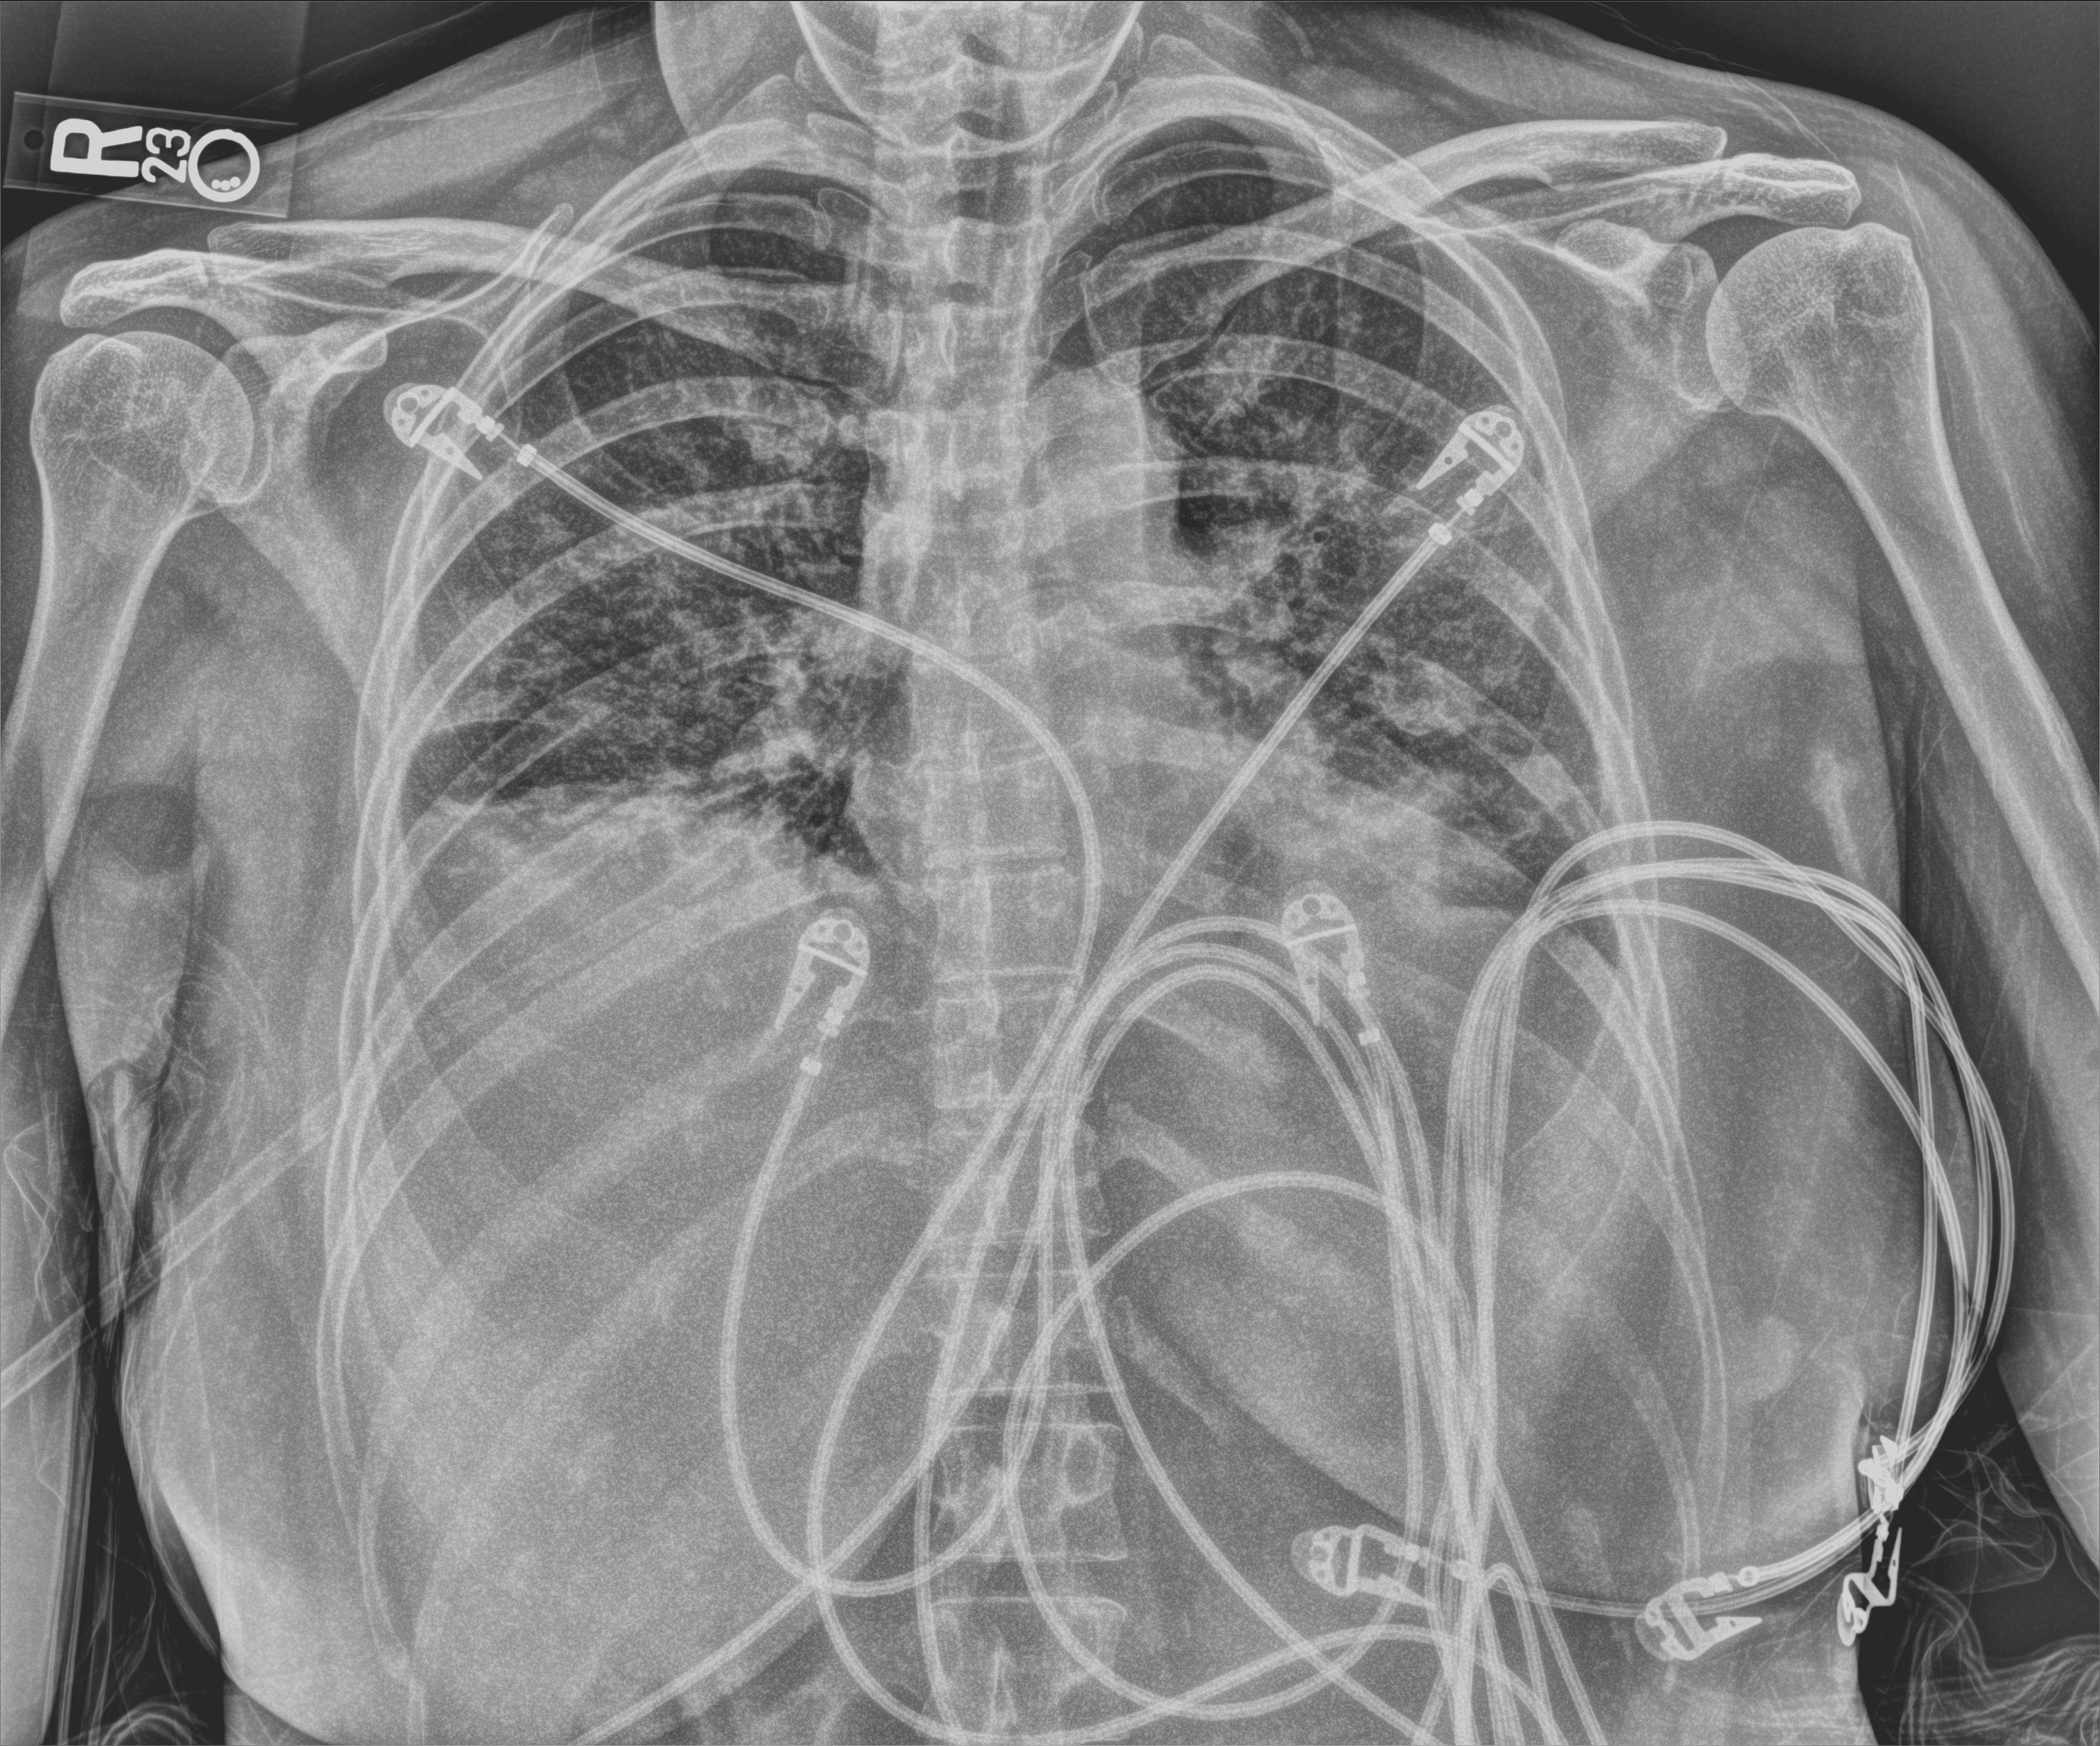
Chest X-ray (portable). Female patient hospitalised with COVID-19, age 18–59 years.
From the hospital-stay record, not from the radiograph (when in the stay this image was taken is not recorded): admitted to intensive care during this hospital stay: yes; diabetes (admission record): no; mechanically ventilated during this hospital stay: no.